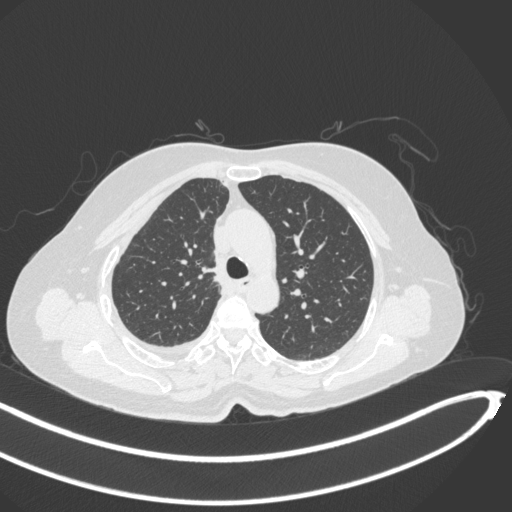
Chest CT, one axial slice. Position 215 of 297 along the scan axis. Reconstruction kernel B31f. 120 kVp. Lung window (W 1500 / L -600 HU). 512 × 512 image matrix. Female patient, age 64 years. From the clinical record (not read from this slice): clinical TNM (as recorded): T1b N0 M1.
Structures marked on this image (rectangle marked by the reading radiologist):
- lung tumour (recorded histology: adenocarcinoma): bounding box <200,259,217,282> (left, top, right, bottom; pixels)